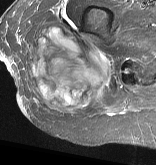
MRI of an extremity soft-tissue mass, one axial slice. Position 21 of 57 along the scan axis. STIR. MR volume resampled by the dataset authors to the PET/CT grid (not the native acquisition matrix). 156 × 165 image matrix, field of view 152 × 161 mm. Female patient. Case-level facts recorded for this patient, not image findings: histological type: epithelioid sarcoma with vascular differentiation; site of the primary tumour: right buttock.
Structures marked on this image (expert contour drawn on MRI and transferred to this co-registered scan by the dataset authors):
- gross tumour volume (mass): bounding box [x1, y1, x2, y2] px = [26, 23, 112, 115]